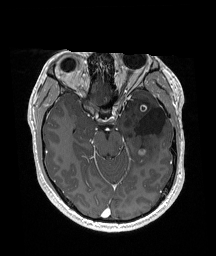
Brain MRI from a brain-tumour surgery series, one axial slice. Slice 111 of 192 in the series (ordered by position). T1-weighted post-contrast. 1 mm slice thickness. 216 × 256 image matrix, field of view 211 × 250 mm. Case-level facts recorded for this patient, not image findings: histopathology: Glioneuronal tumor; WHO grade: 2.
Annotated regions visible in this slice (expert manual segmentation):
- previous resection cavity: box from (x=135, y=107) to (x=166, y=135) px
- tumour: (x=138, y=104)–(x=148, y=156)